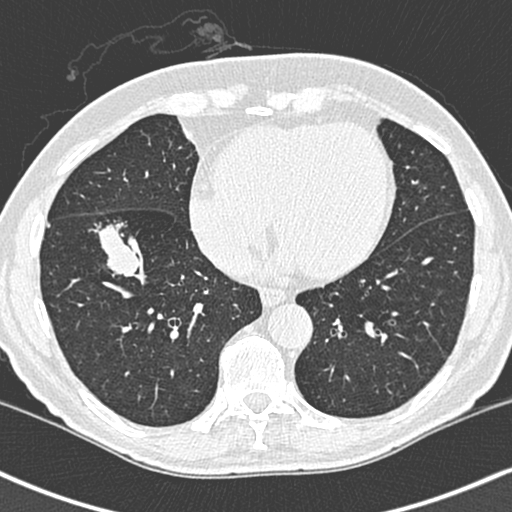
Low-dose screening chest CT, one axial slice. Position 97 of 248 along the scan axis. 120 kVp. Lung window (W 1500 / L -600 HU). 1.3 mm slice thickness. 512 × 512 image matrix, field of view 323 × 323 mm.
Structures marked on this image (manually delineated by an expert):
- lesion 1 (tumor, lower lobe of right lung): bounding box [x1, y1, x2, y2] px = [99, 184, 141, 239]